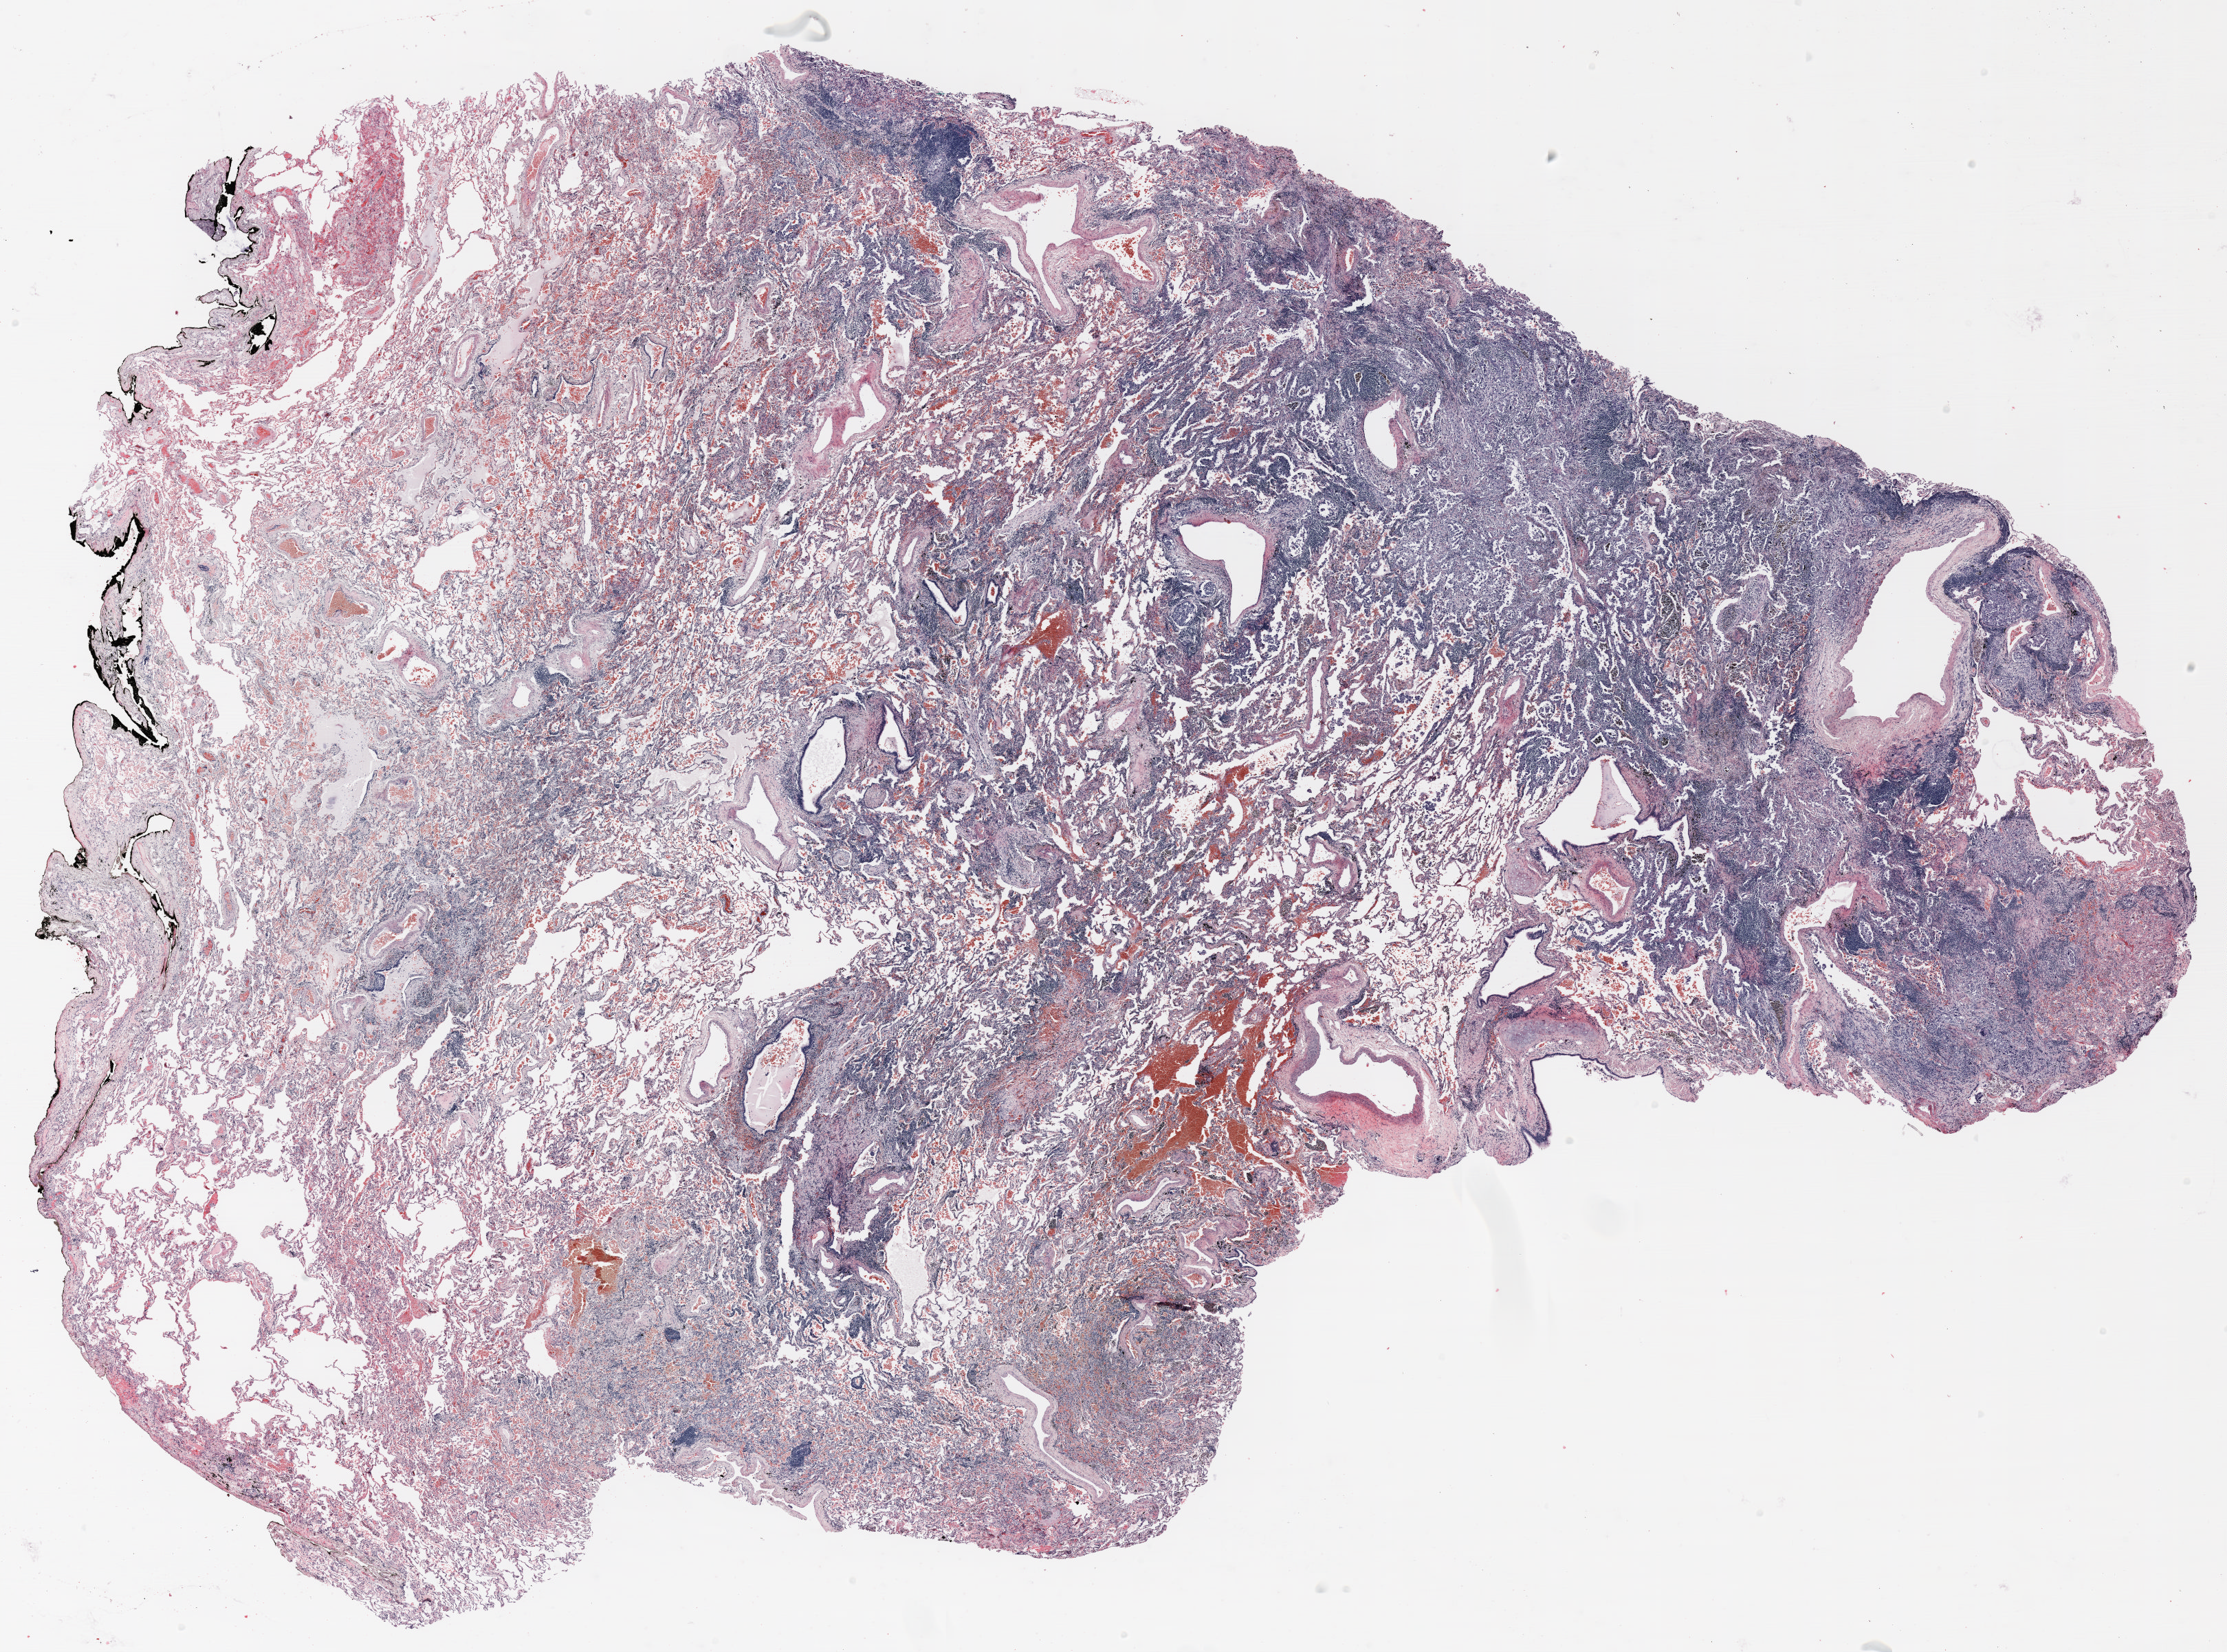
Hematoxylin and eosin (H&E) stained whole-slide image, shown as a low-resolution overview of the whole scanned area (about 26.0 x 19.3 mm, acquisition: 20x scan), formalin-fixed paraffin-embedded (FFPE) section, lung. Male, age 70 at enrolment. Current smoker at enrolment. Grade: moderately differentiated (G2).
Primary tumour location (clinical record): left upper lobe. Participant's lung-cancer diagnosis: Adenocarcinoma, NOS (ICD-O-3 8140/3). Stage (AJCC 6th edition): IIIA. Tumour size (pathology): 17 mm. ICD-O-3 topography: upper lobe of lung (C34.1).